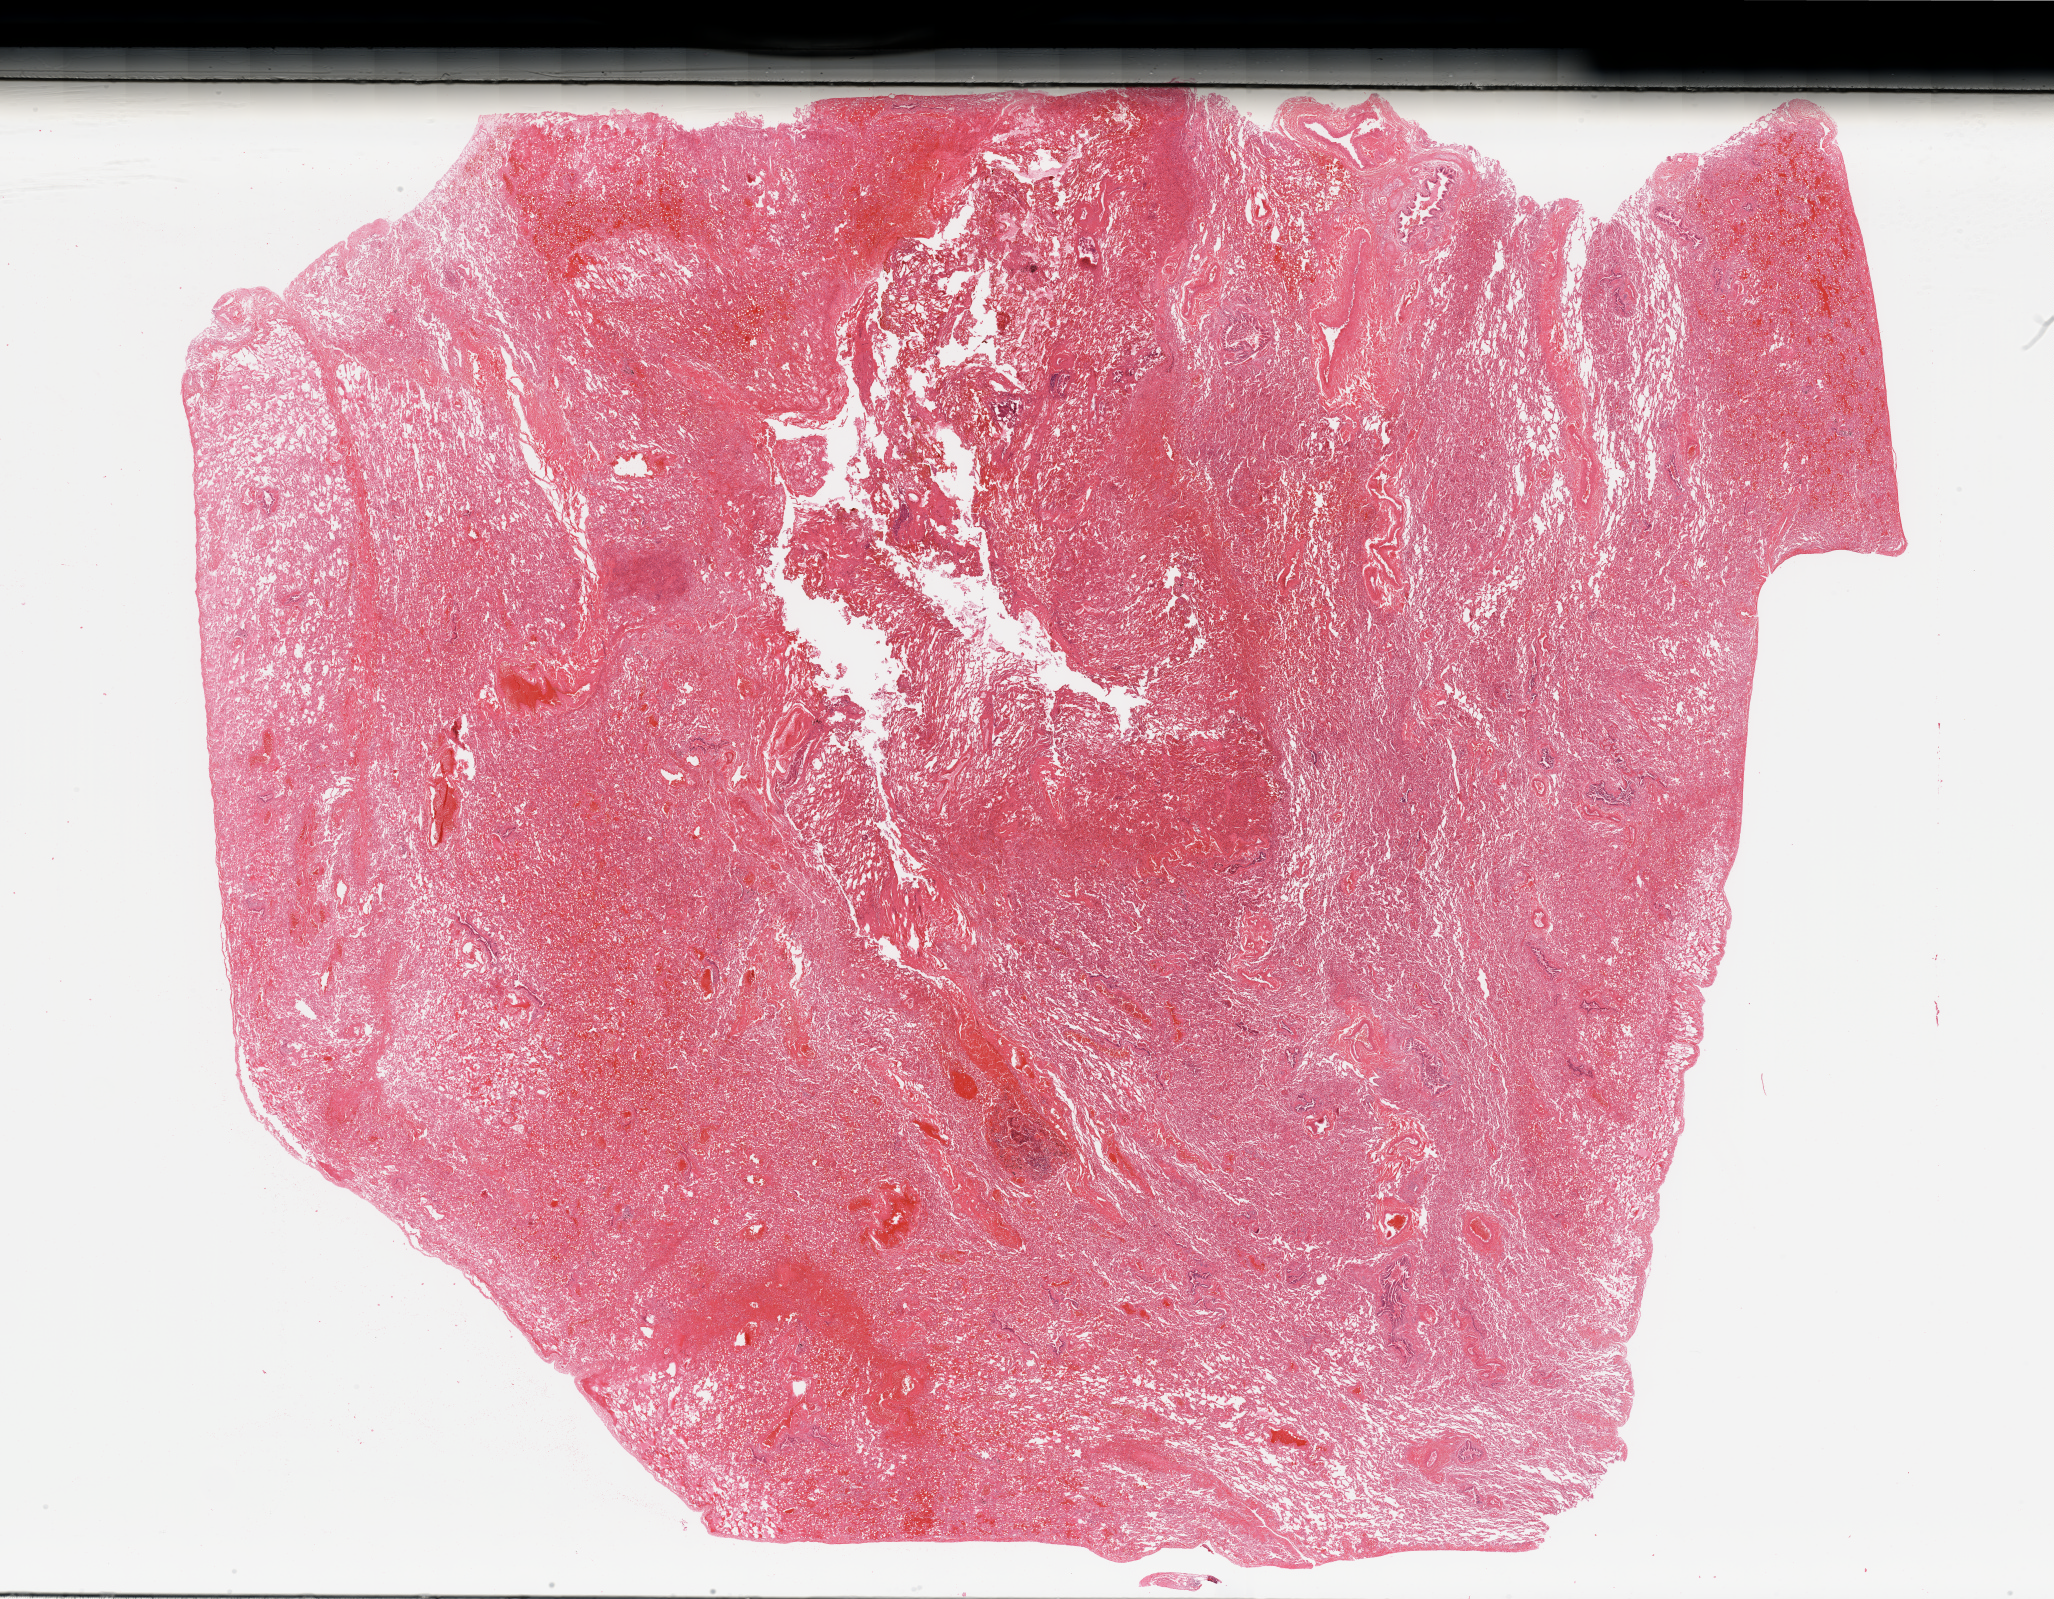
Digitized H&E tissue section (whole slide), a low-resolution overview of the entire scanned area, about 32.5 x 25.3 mm. Normal (non-tumour) tissue sample, lung. Patient: female, age 25 years.
This section: normal (non-tumour) tissue from the same patient. Patient diagnosis: Adenocarcinoma, NOS.